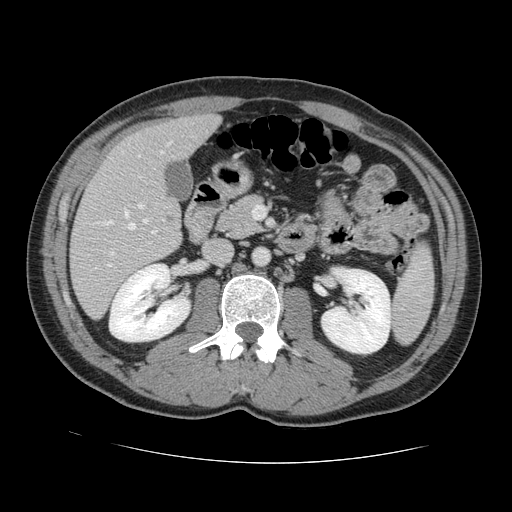
Contrast-enhanced abdominal CT, one axial slice; slice 59 of 131 in the series (ordered by position); soft-tissue window (W 400 / L 40 HU); 512 × 512 image matrix, field of view 380 × 380 mm. Male patient, age 40 years. From the clinical record (not read from this slice): diagnosis: colorectal cancer liver metastases, imaged before liver resection; multiple liver metastases: yes; largest metastasis: 2.9 cm; disease in both lobes: yes.
Structures marked on this image (outlined manually by an expert reader):
- hepatic veins: bounding box (x1, y1, x2, y2) in pixels: (96, 141, 173, 255)
- liver: (71, 115, 218, 317)
- planned liver remnant (the part of the liver to remain after resection): (112, 116, 218, 177)
- portal vein (with intrahepatic branches): (107, 155, 157, 267)
- liver metastasis: (167, 217, 174, 223)